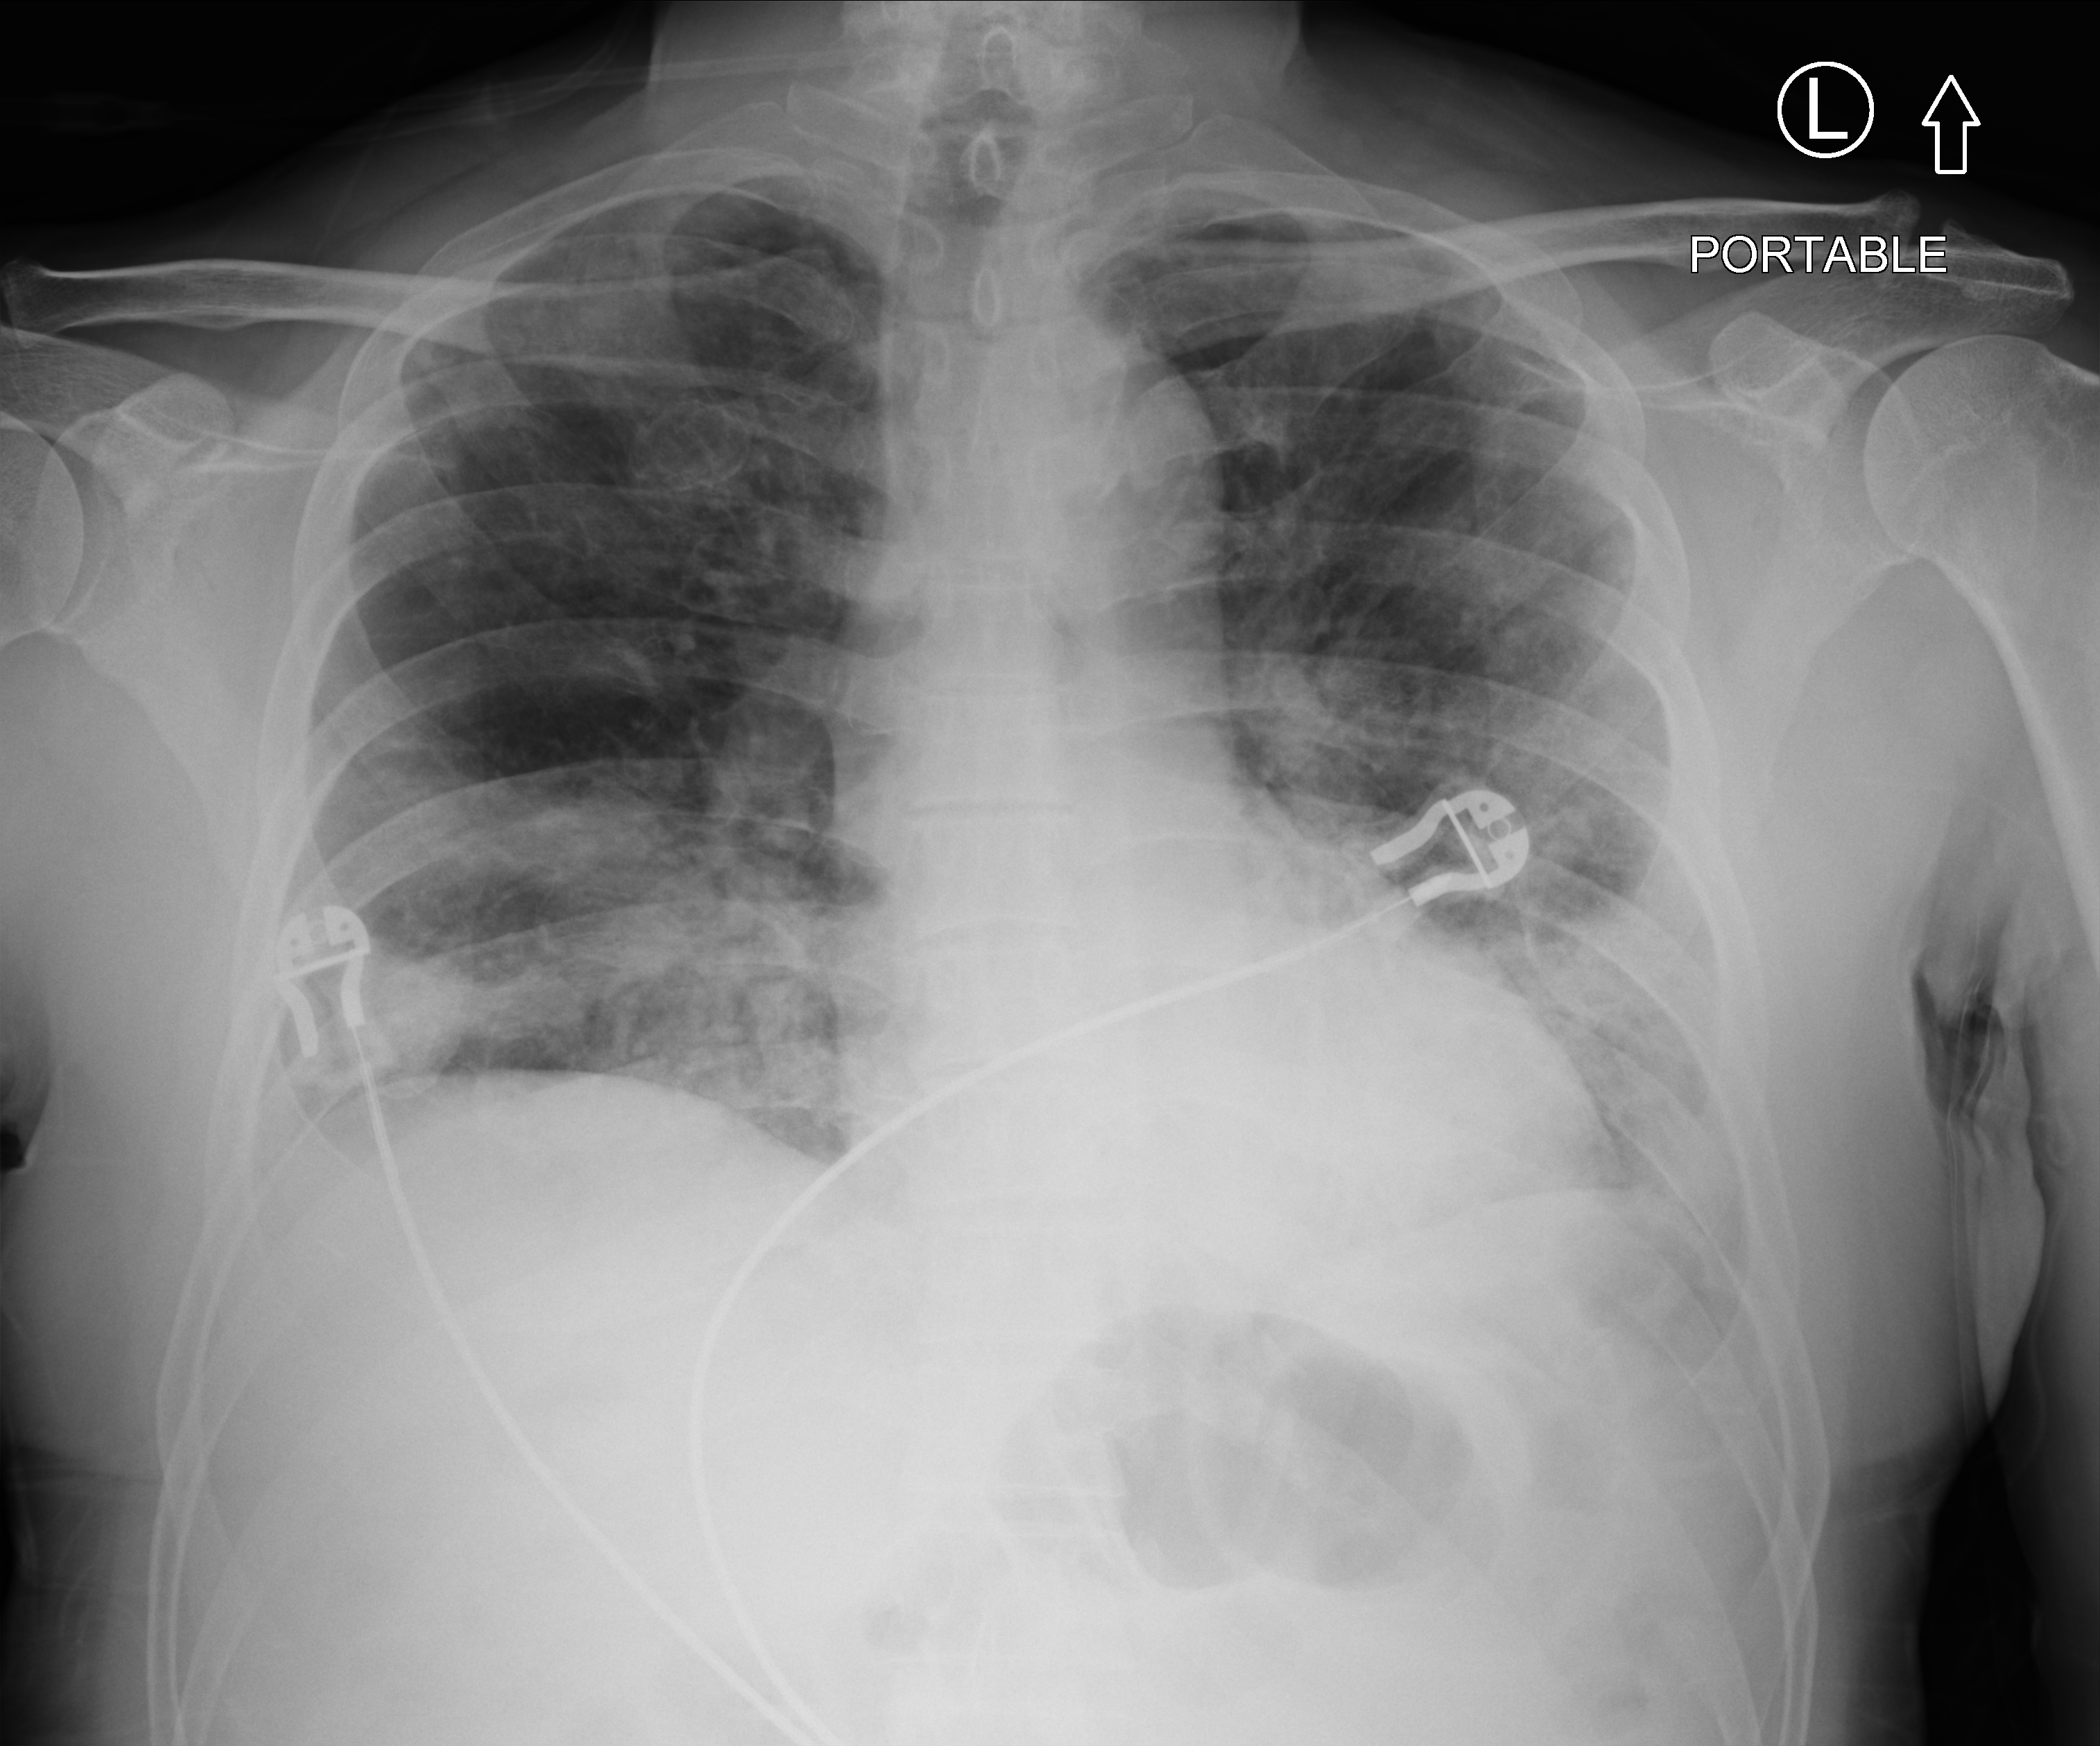
Portable chest radiograph, anteroposterior (AP) projection. Patient hospitalised with COVID-19; male, aged 60–74 years.
From the hospital-stay record, not from the radiograph (when in the stay this image was taken is not recorded):
- mechanically ventilated during this hospital stay: yes
- admitted to intensive care during this hospital stay: yes